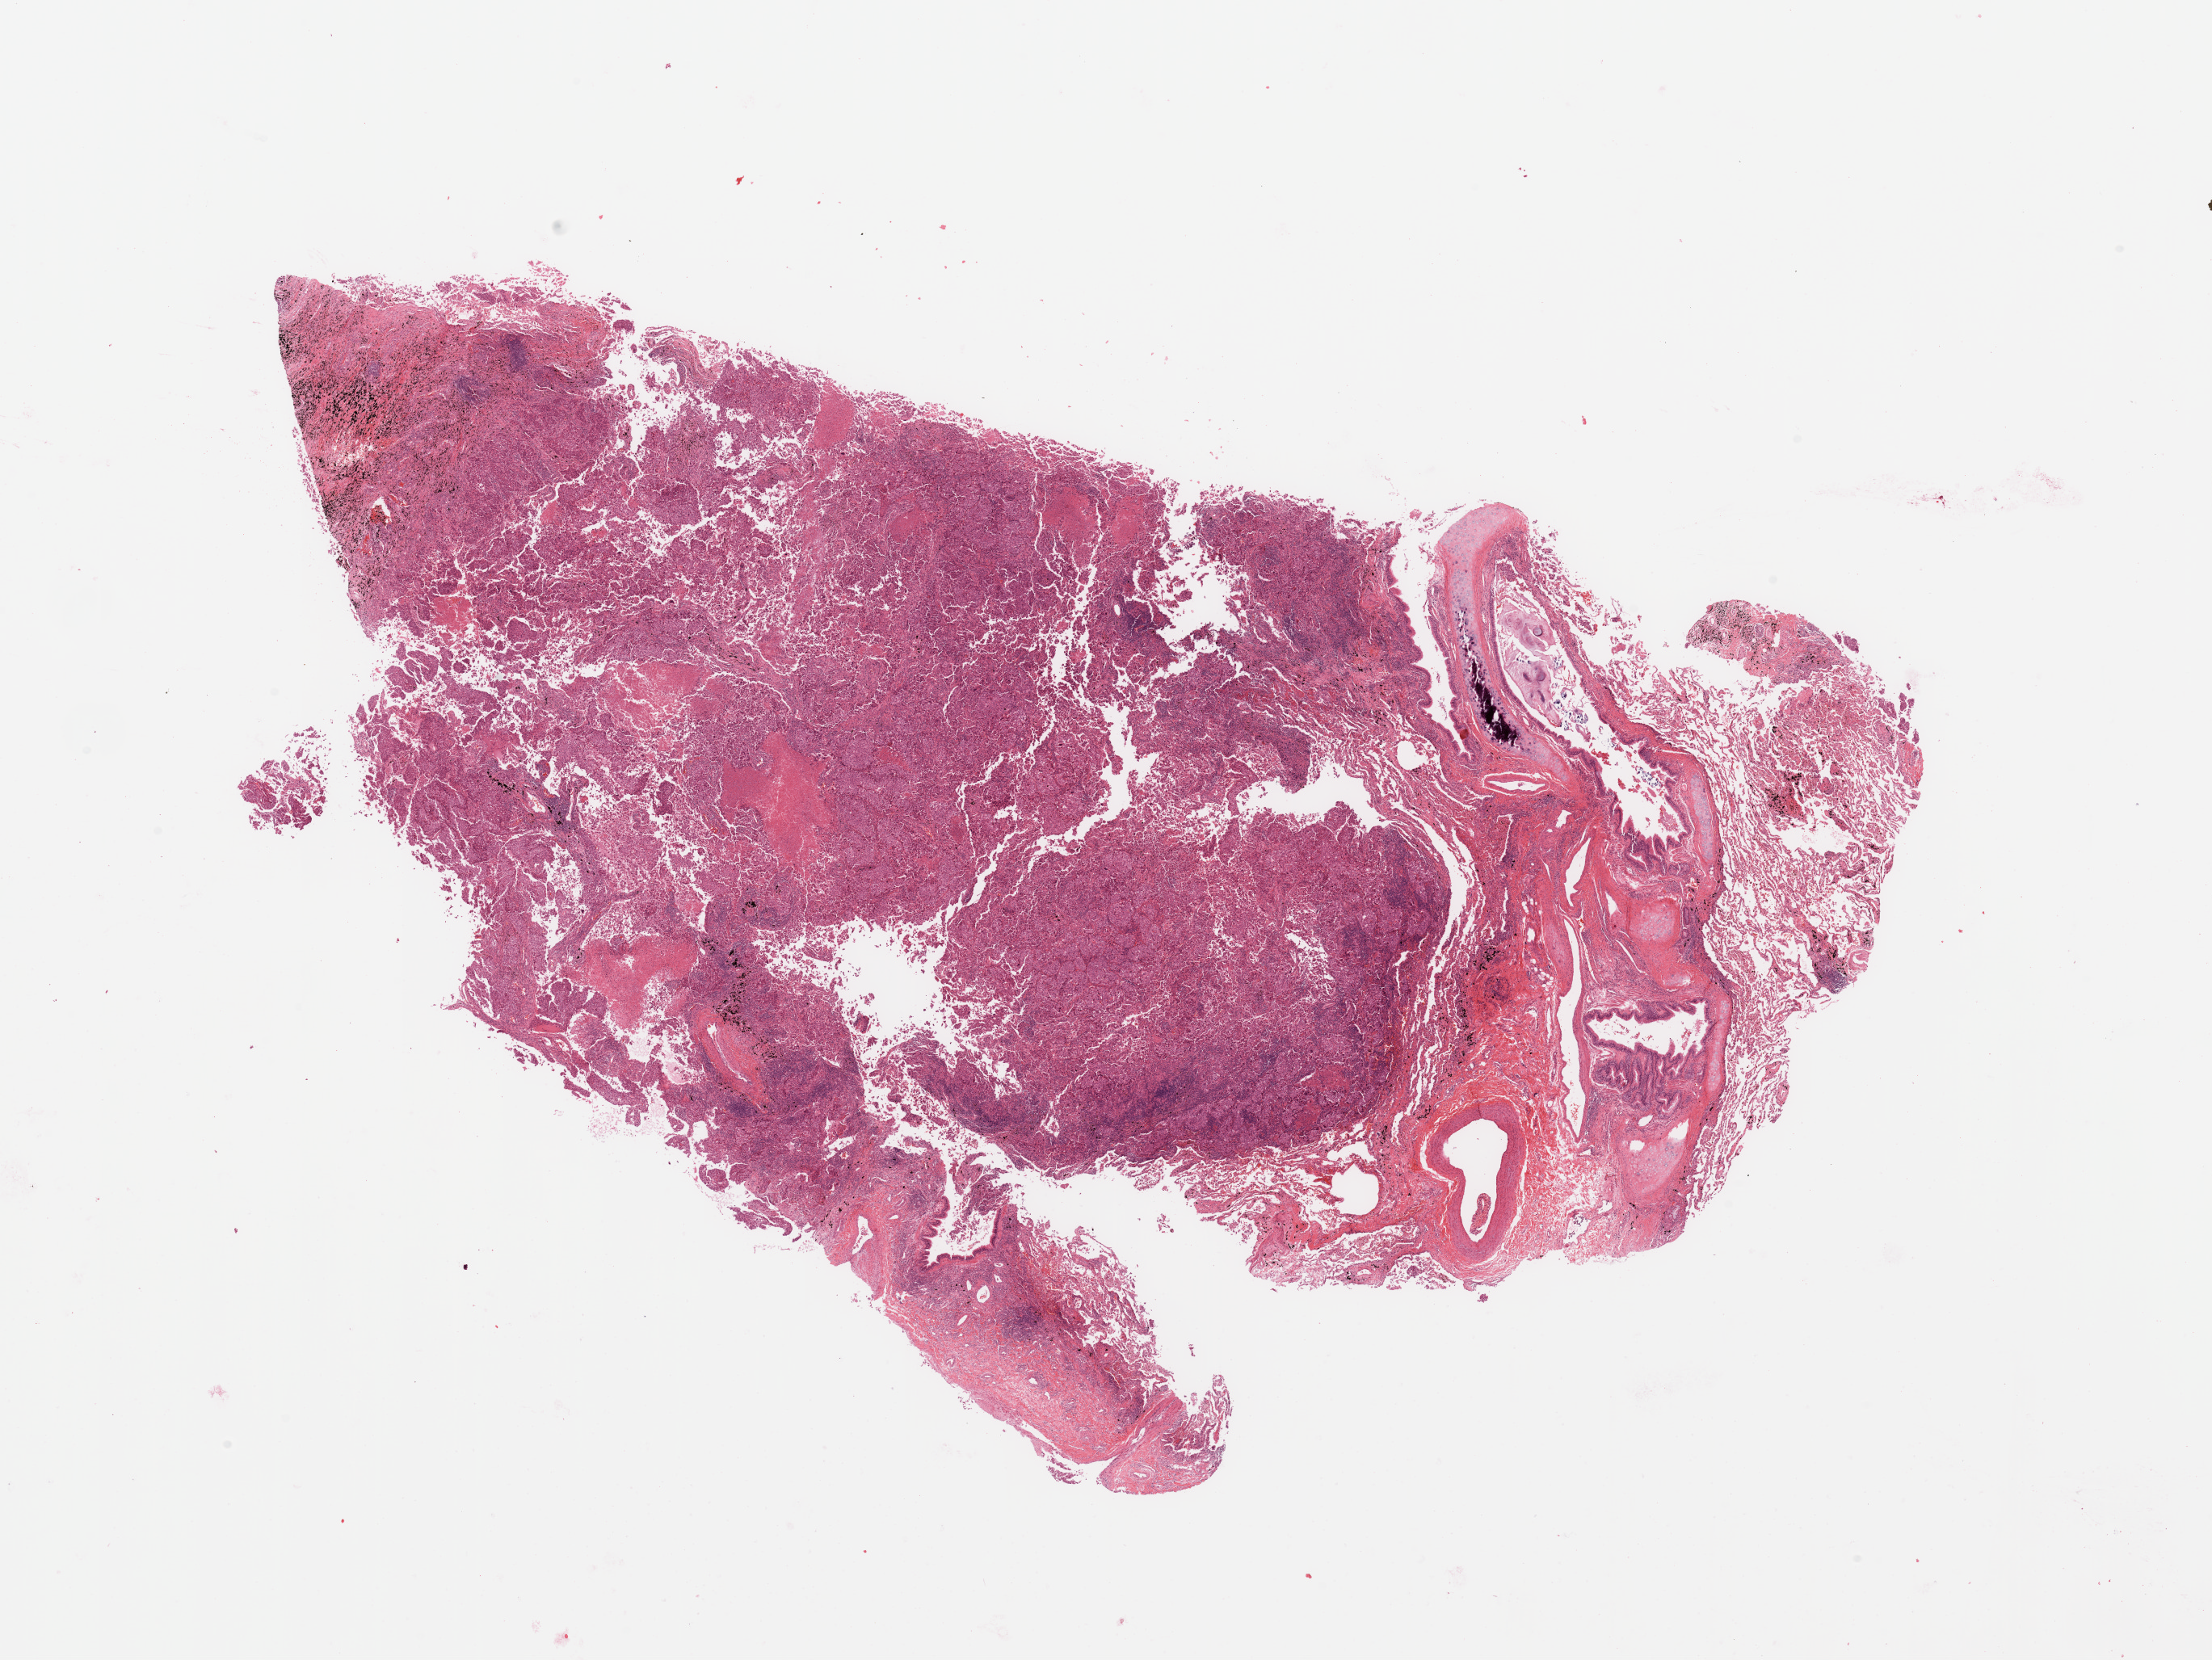
Whole-slide histology image, H&E-stained — whole scanned area (about 21.7 x 16.3 mm) shown as a low-resolution overview, lung, tumour tissue. 59-year-old male patient. Histologic grade: G3 (poorly differentiated).
Primary tumour site (as recorded): right upper lobe. AJCC pathologic stage: IB. Diagnosis: Adenocarcinoma, NOS.